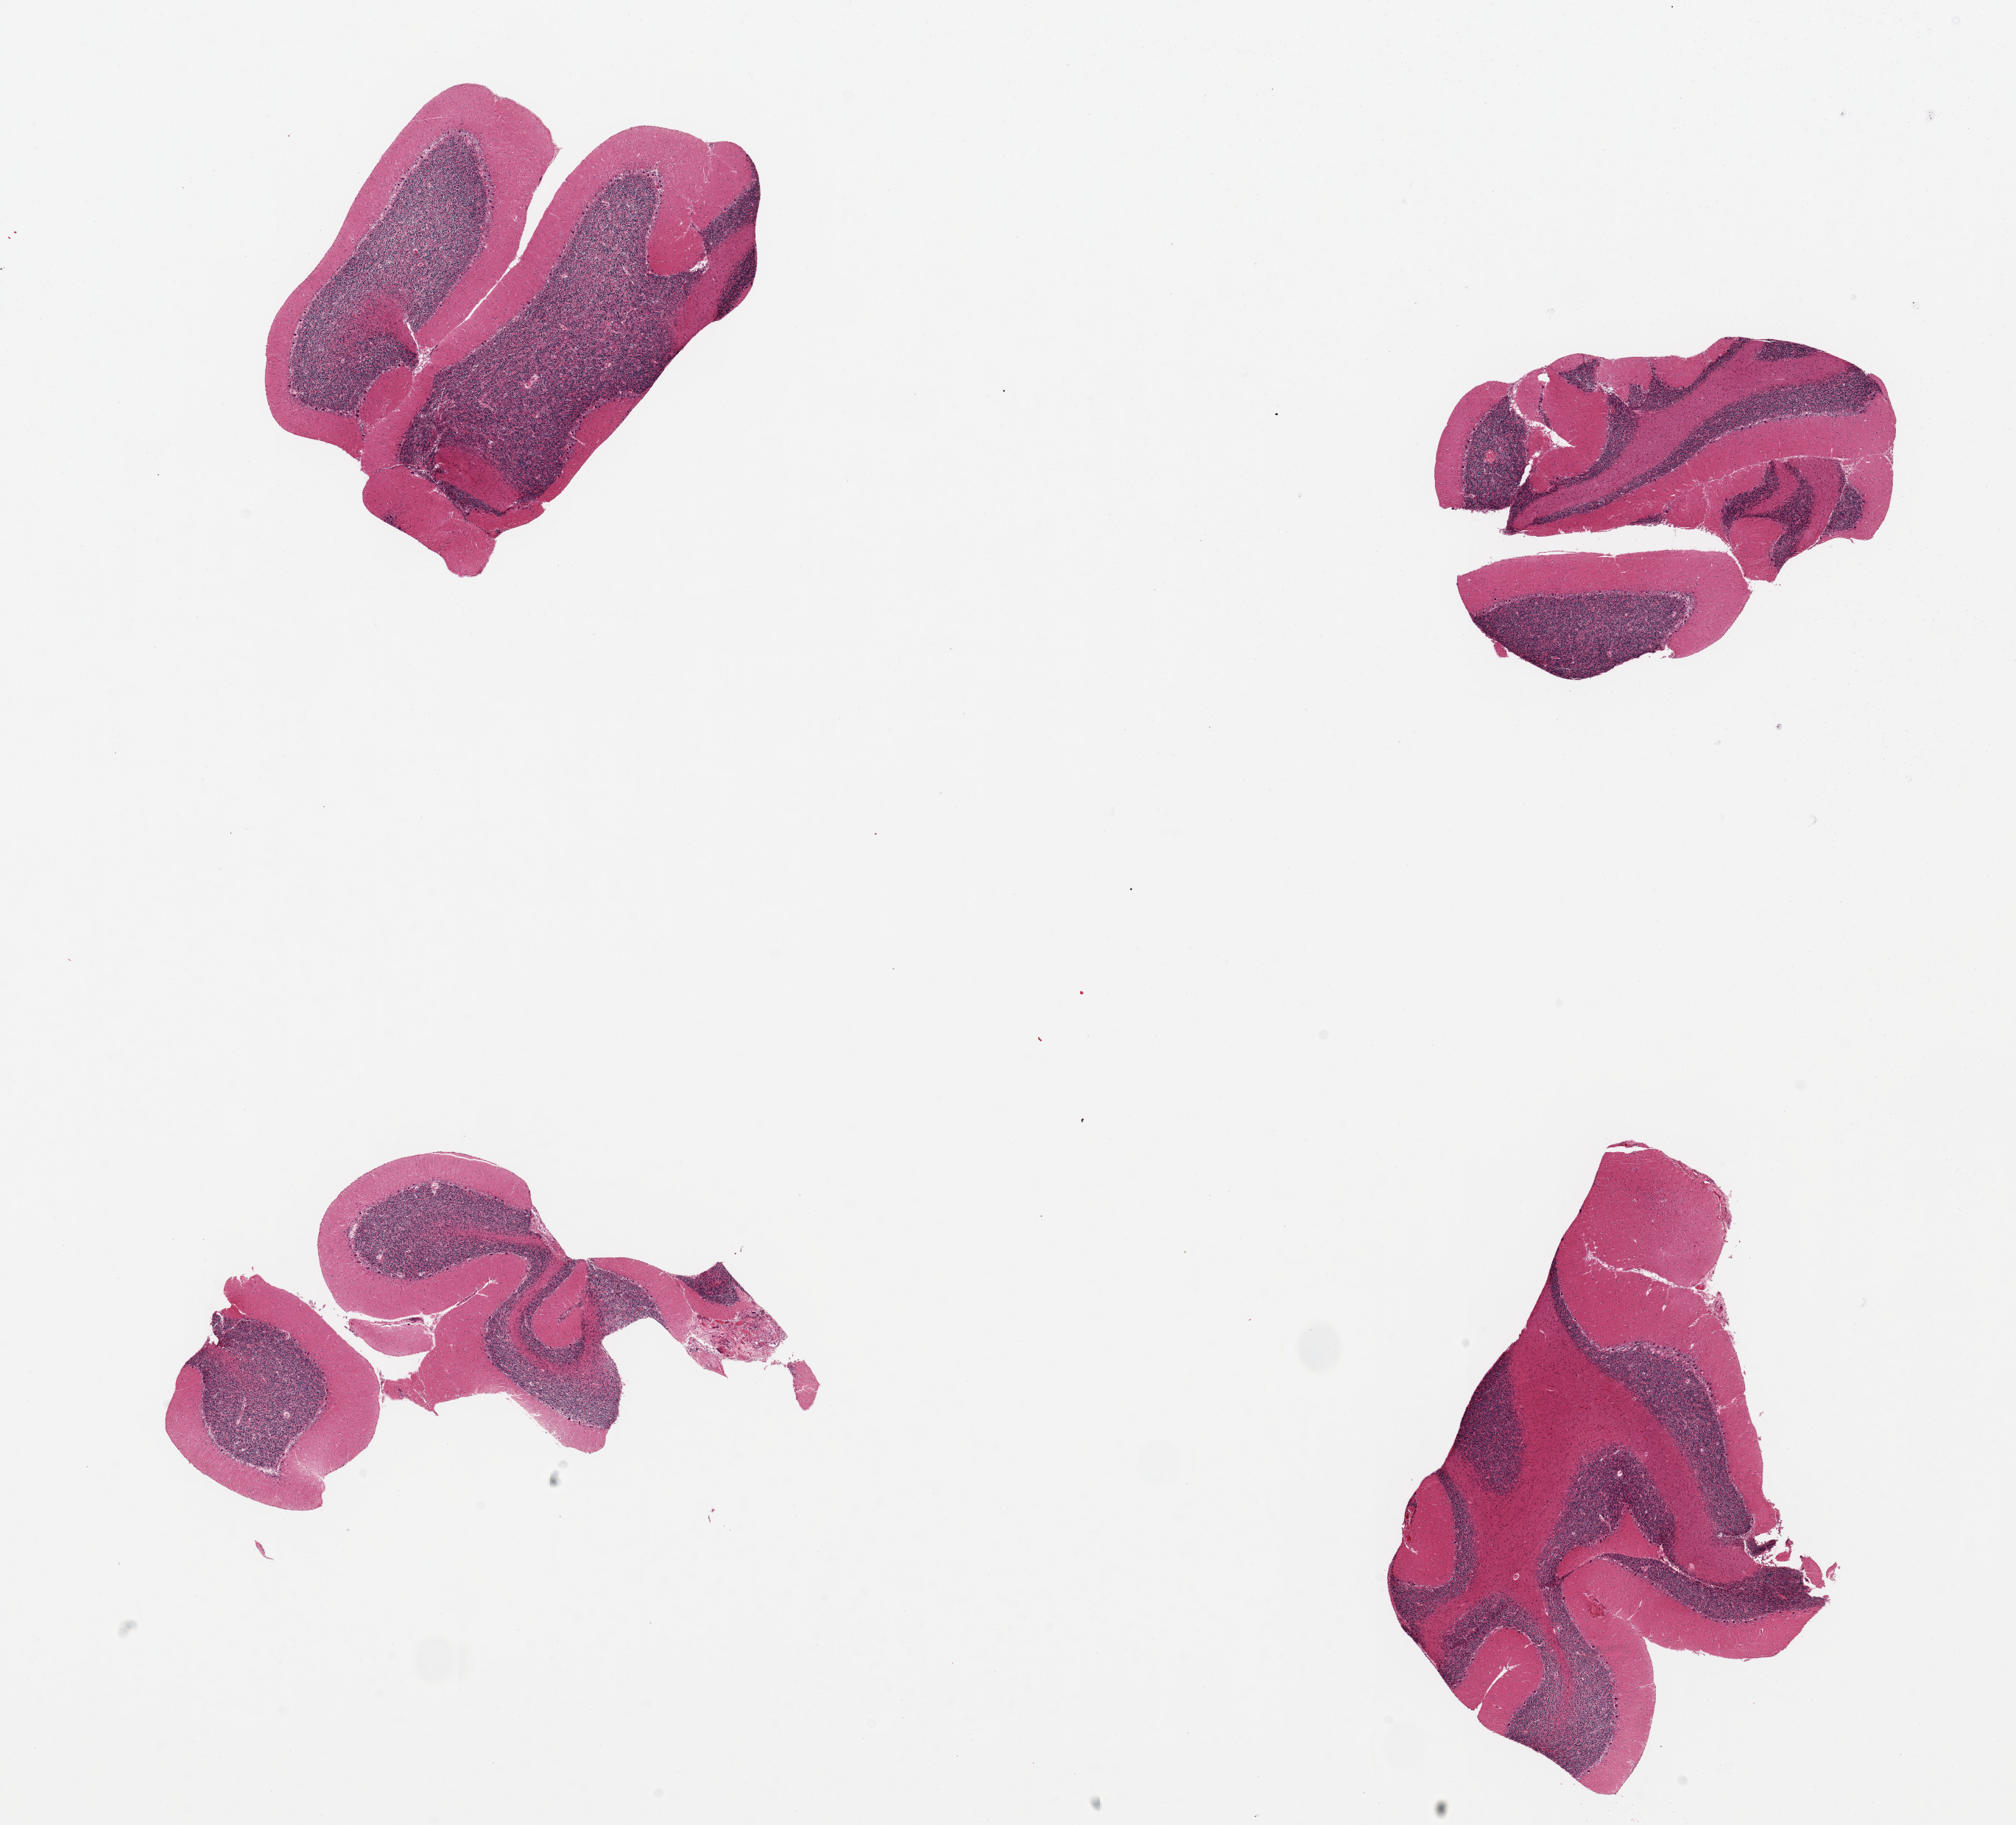
Digitized haematoxylin and eosin-stained section — whole scanned area (about 21.7 x 19.6 mm, acquisition: 20x scan) shown as a low-resolution overview; PAXgene-fixed, paraffin-embedded tissue; target tissue: cerebellum; tissue donor sample. Female donor.
* review note (as recorded): 4 pieces, some suggestion of hypoxic damage